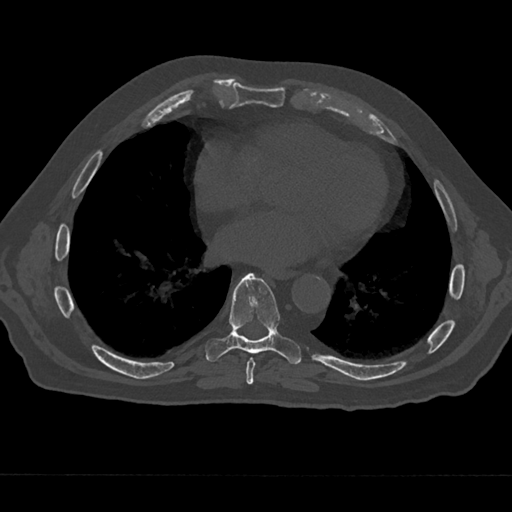
CT including the spine, one axial slice; position 323 of 797 along the scan axis; reconstruction kernel Br40s/3; bone window (W 1800 / L 400 HU); 0.5 mm slice thickness; 512 × 512 image matrix, field of view 377 × 377 mm. Patient: male, 75 years. Case-level facts recorded for this patient, not image findings: primary cancer: renal; vertebrae with lytic lesions (as recorded): T4.
Outlined on this slice (semi-automatically segmented with operator editing):
- T7 vertebra: bounding box [x1, y1, x2, y2] px = [244, 357, 258, 385]
- T8 vertebra: [205, 273, 301, 365]